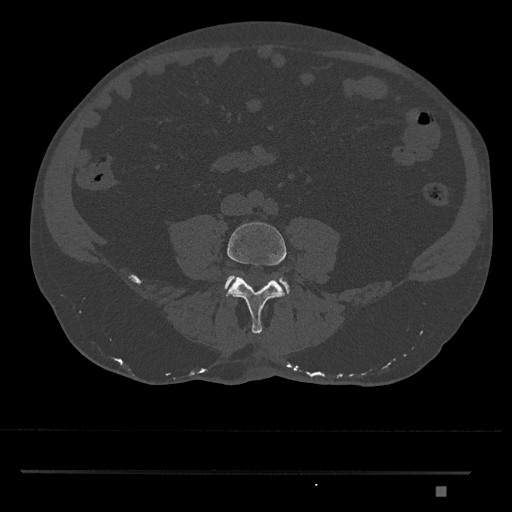
CT including the spine, one axial slice; position 603 of 1134 along the scan axis; 120 kVp; bone window (W 1800 / L 400 HU); 0.5 mm slice thickness; 512 × 512 image matrix, field of view 429 × 429 mm. Patient: male, 65 years. From the clinical record (not read from this slice): primary cancer: prostate.
Structures marked on this image (semi-automatic segmentation, software-assisted and operator-edited):
- L4 vertebra: box from (x=226, y=222) to (x=287, y=334) px
- L5 vertebra: (x=224, y=276)–(x=290, y=294)